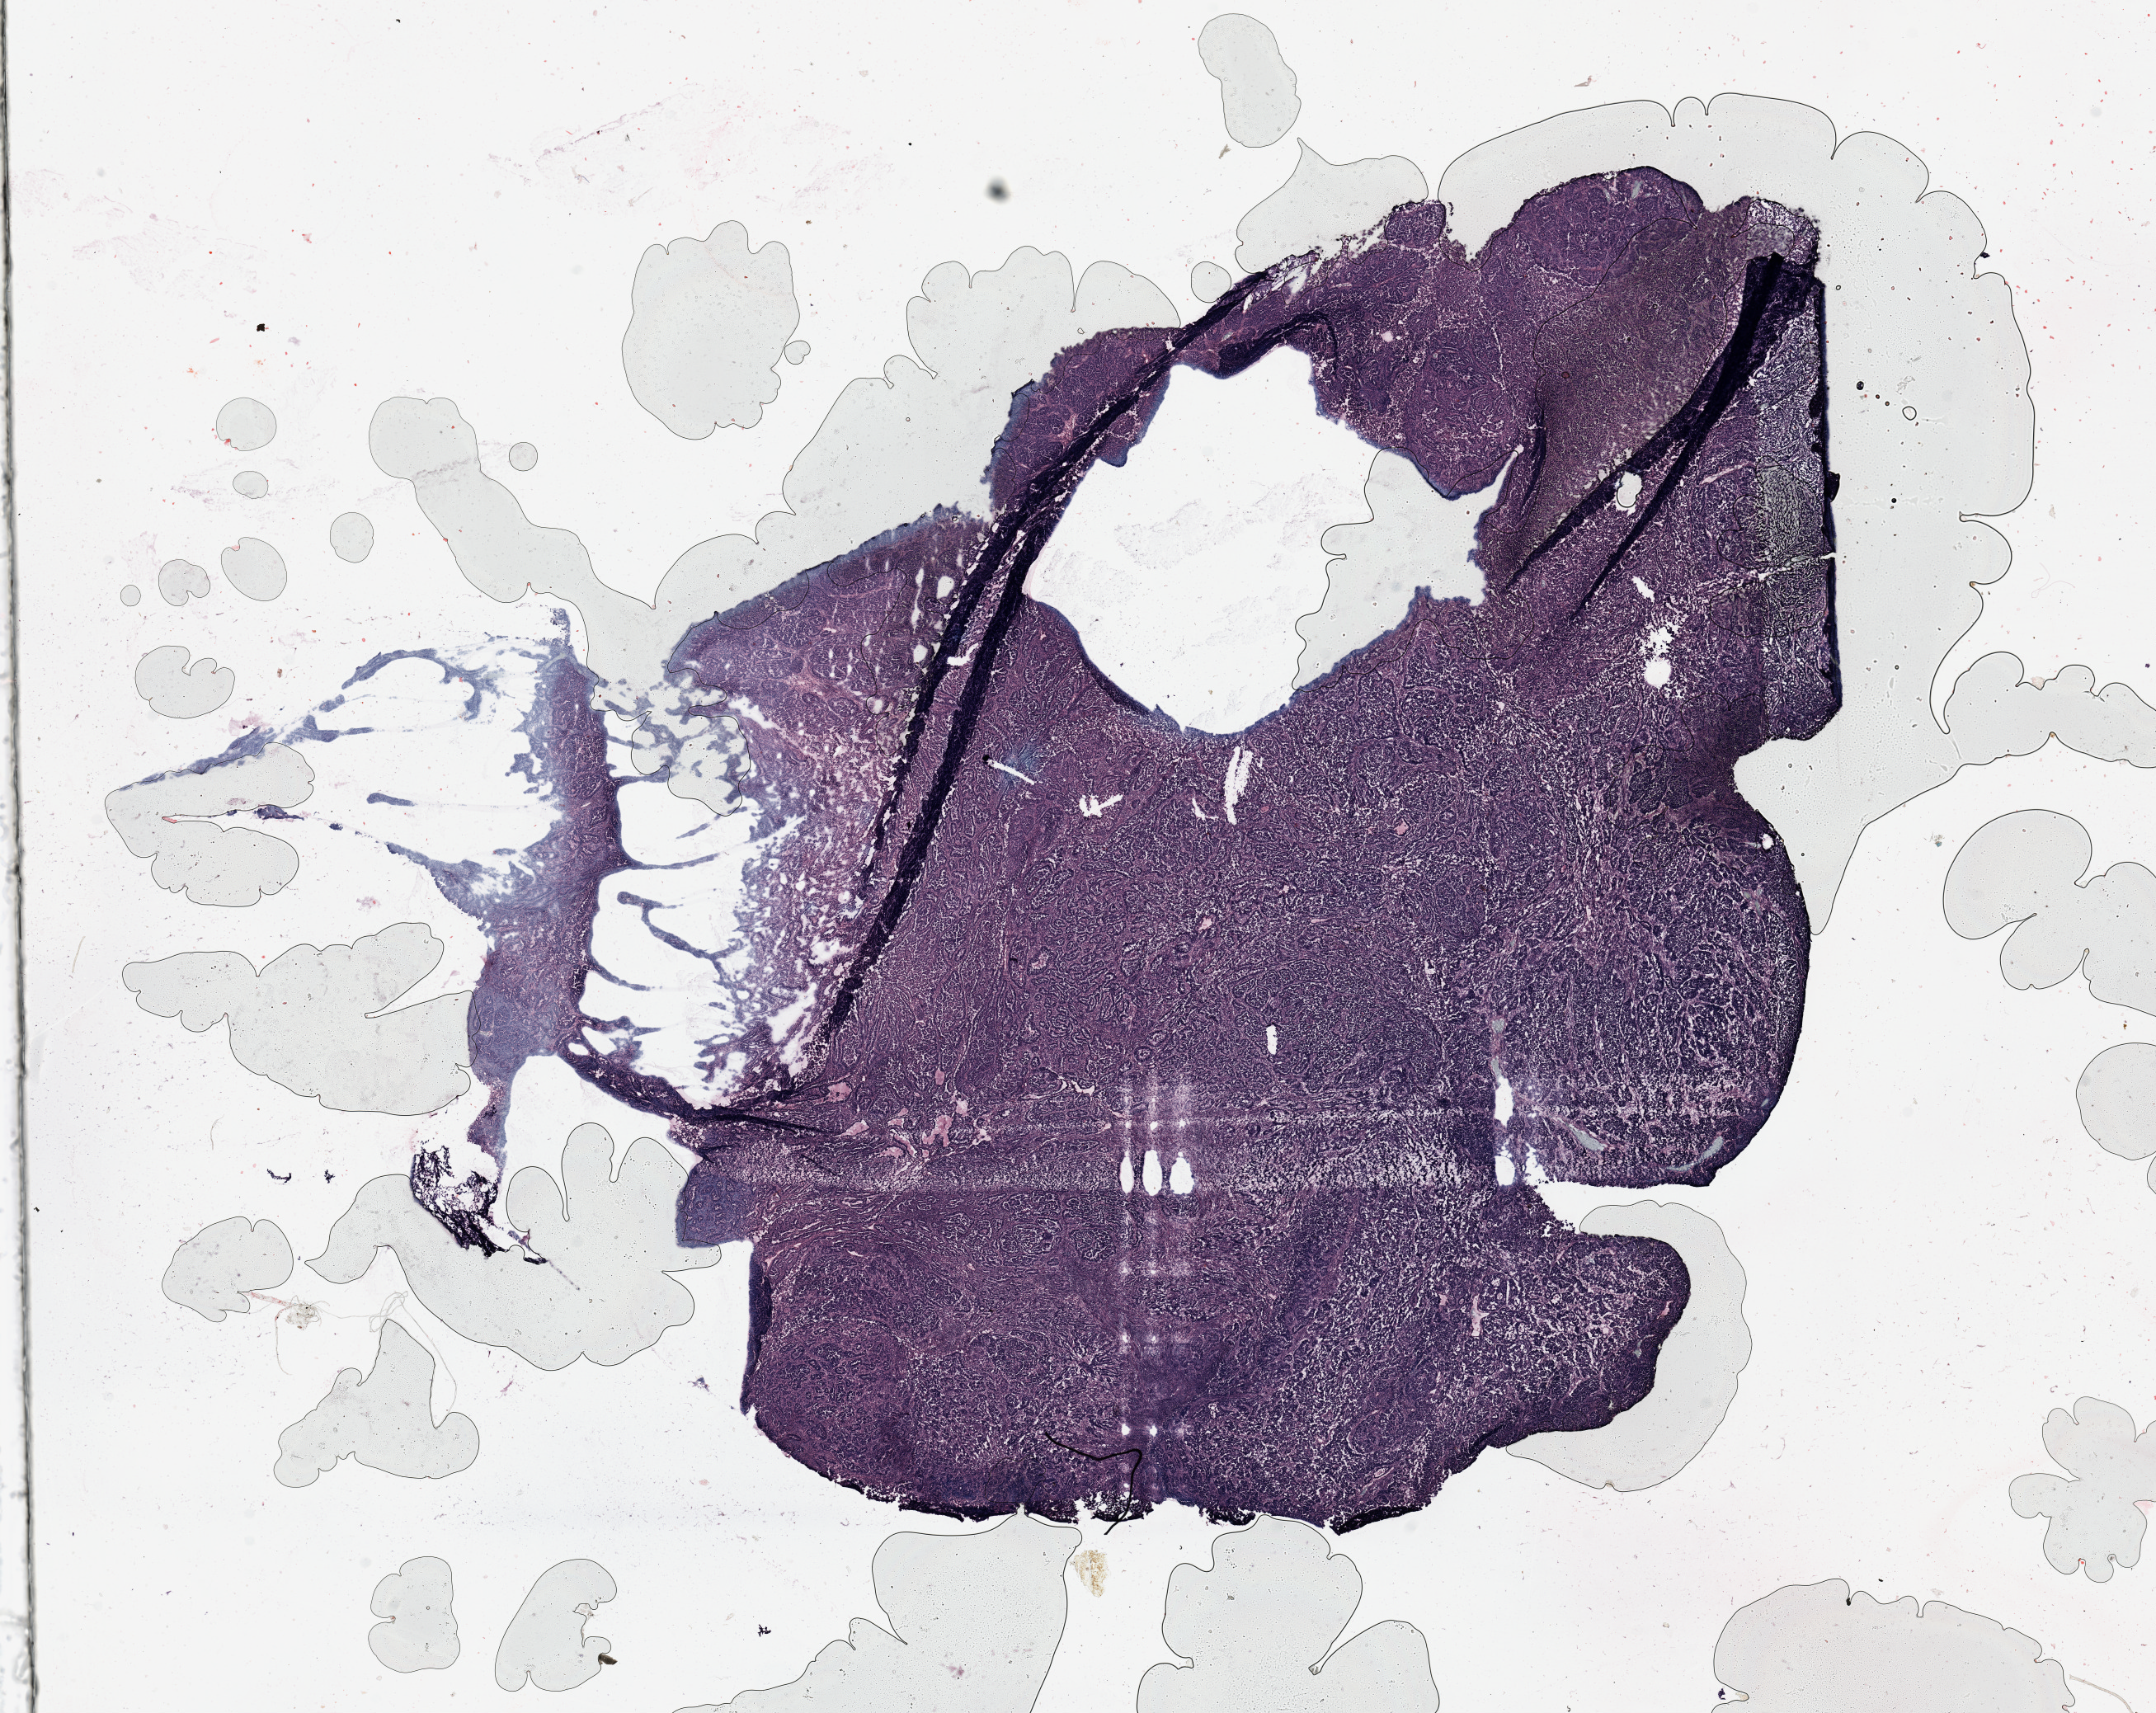
Whole-slide histology image, H&E-stained — low-resolution overview of the scanned area, about 20.7 x 16.4 mm (acquisition: 20x scan). Uterus, tumour tissue. Female, 60 y/o. Histologic grade: G3 (poorly differentiated).
• AJCC pathologic stage: III
• histologic diagnosis: Endometrioid adenocarcinoma, NOS